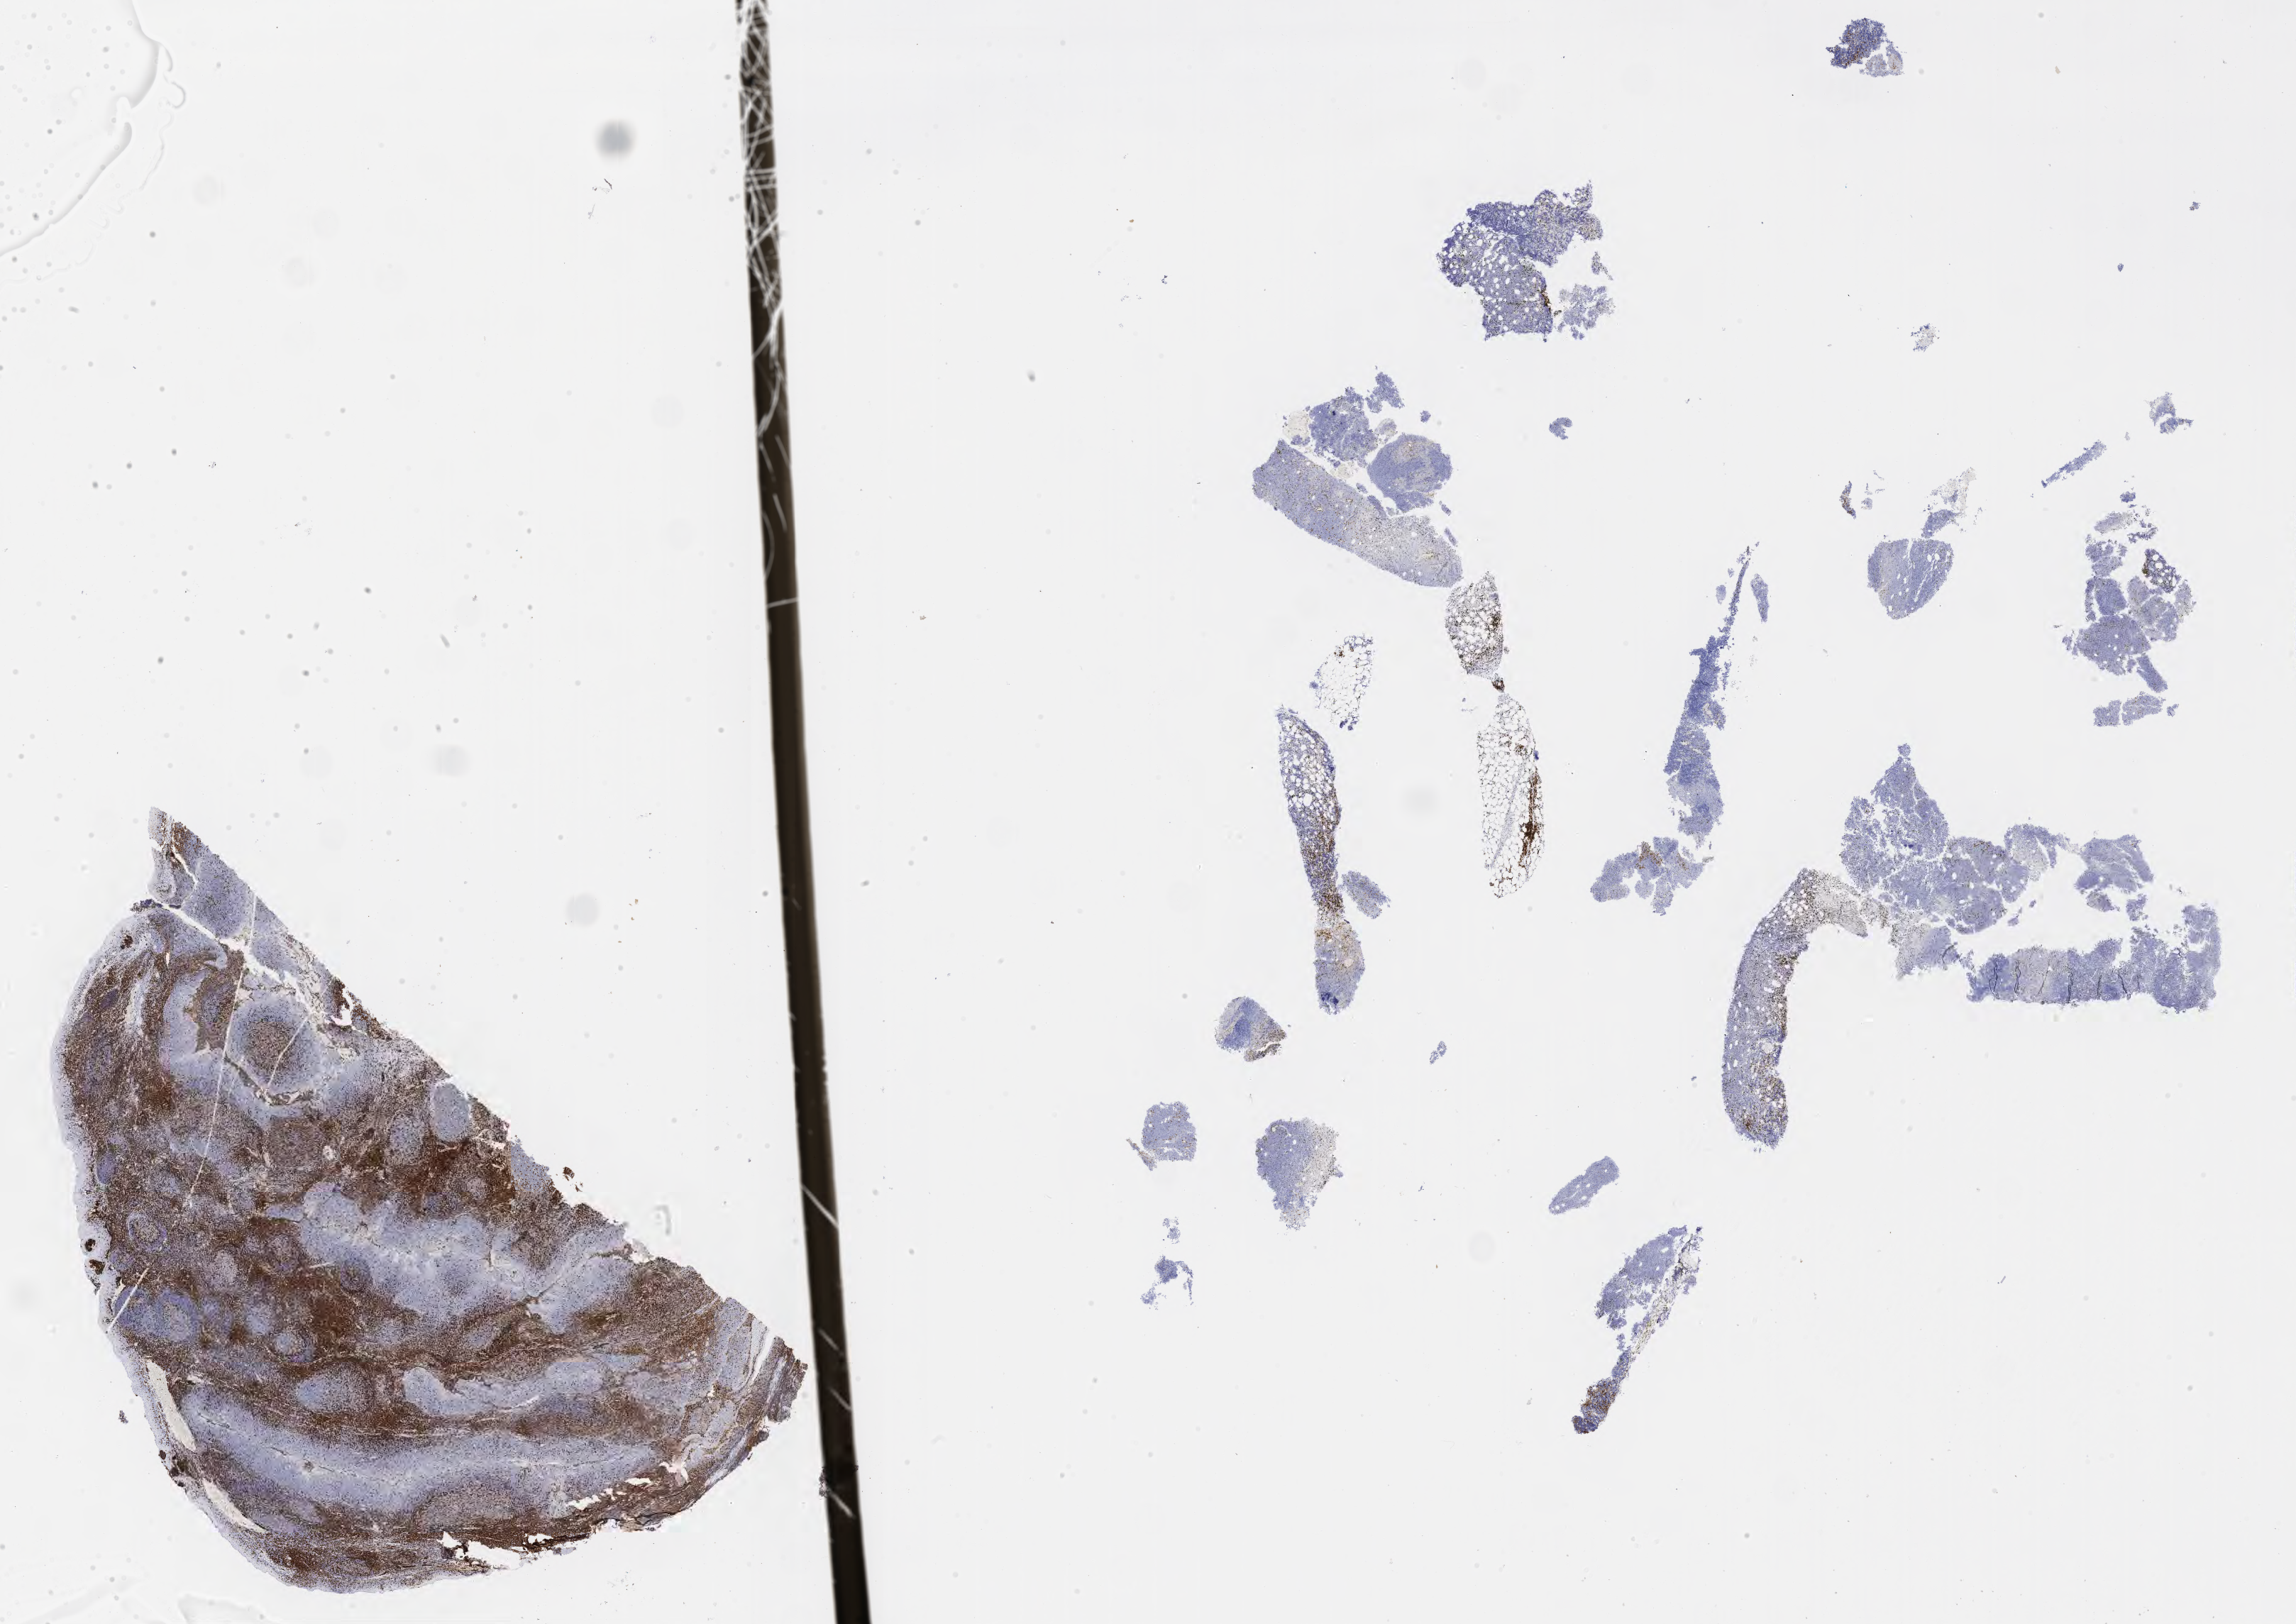
Immunohistochemistry (IHC) whole-slide image stained for CD3, whole scanned area (about 26.2 x 18.5 mm) shown as a low-resolution overview. Specimen: tumor tissue. Site: pelvis. Female patient, age 64 years.
Diagnosis: Burkitt lymphoma, NOS.